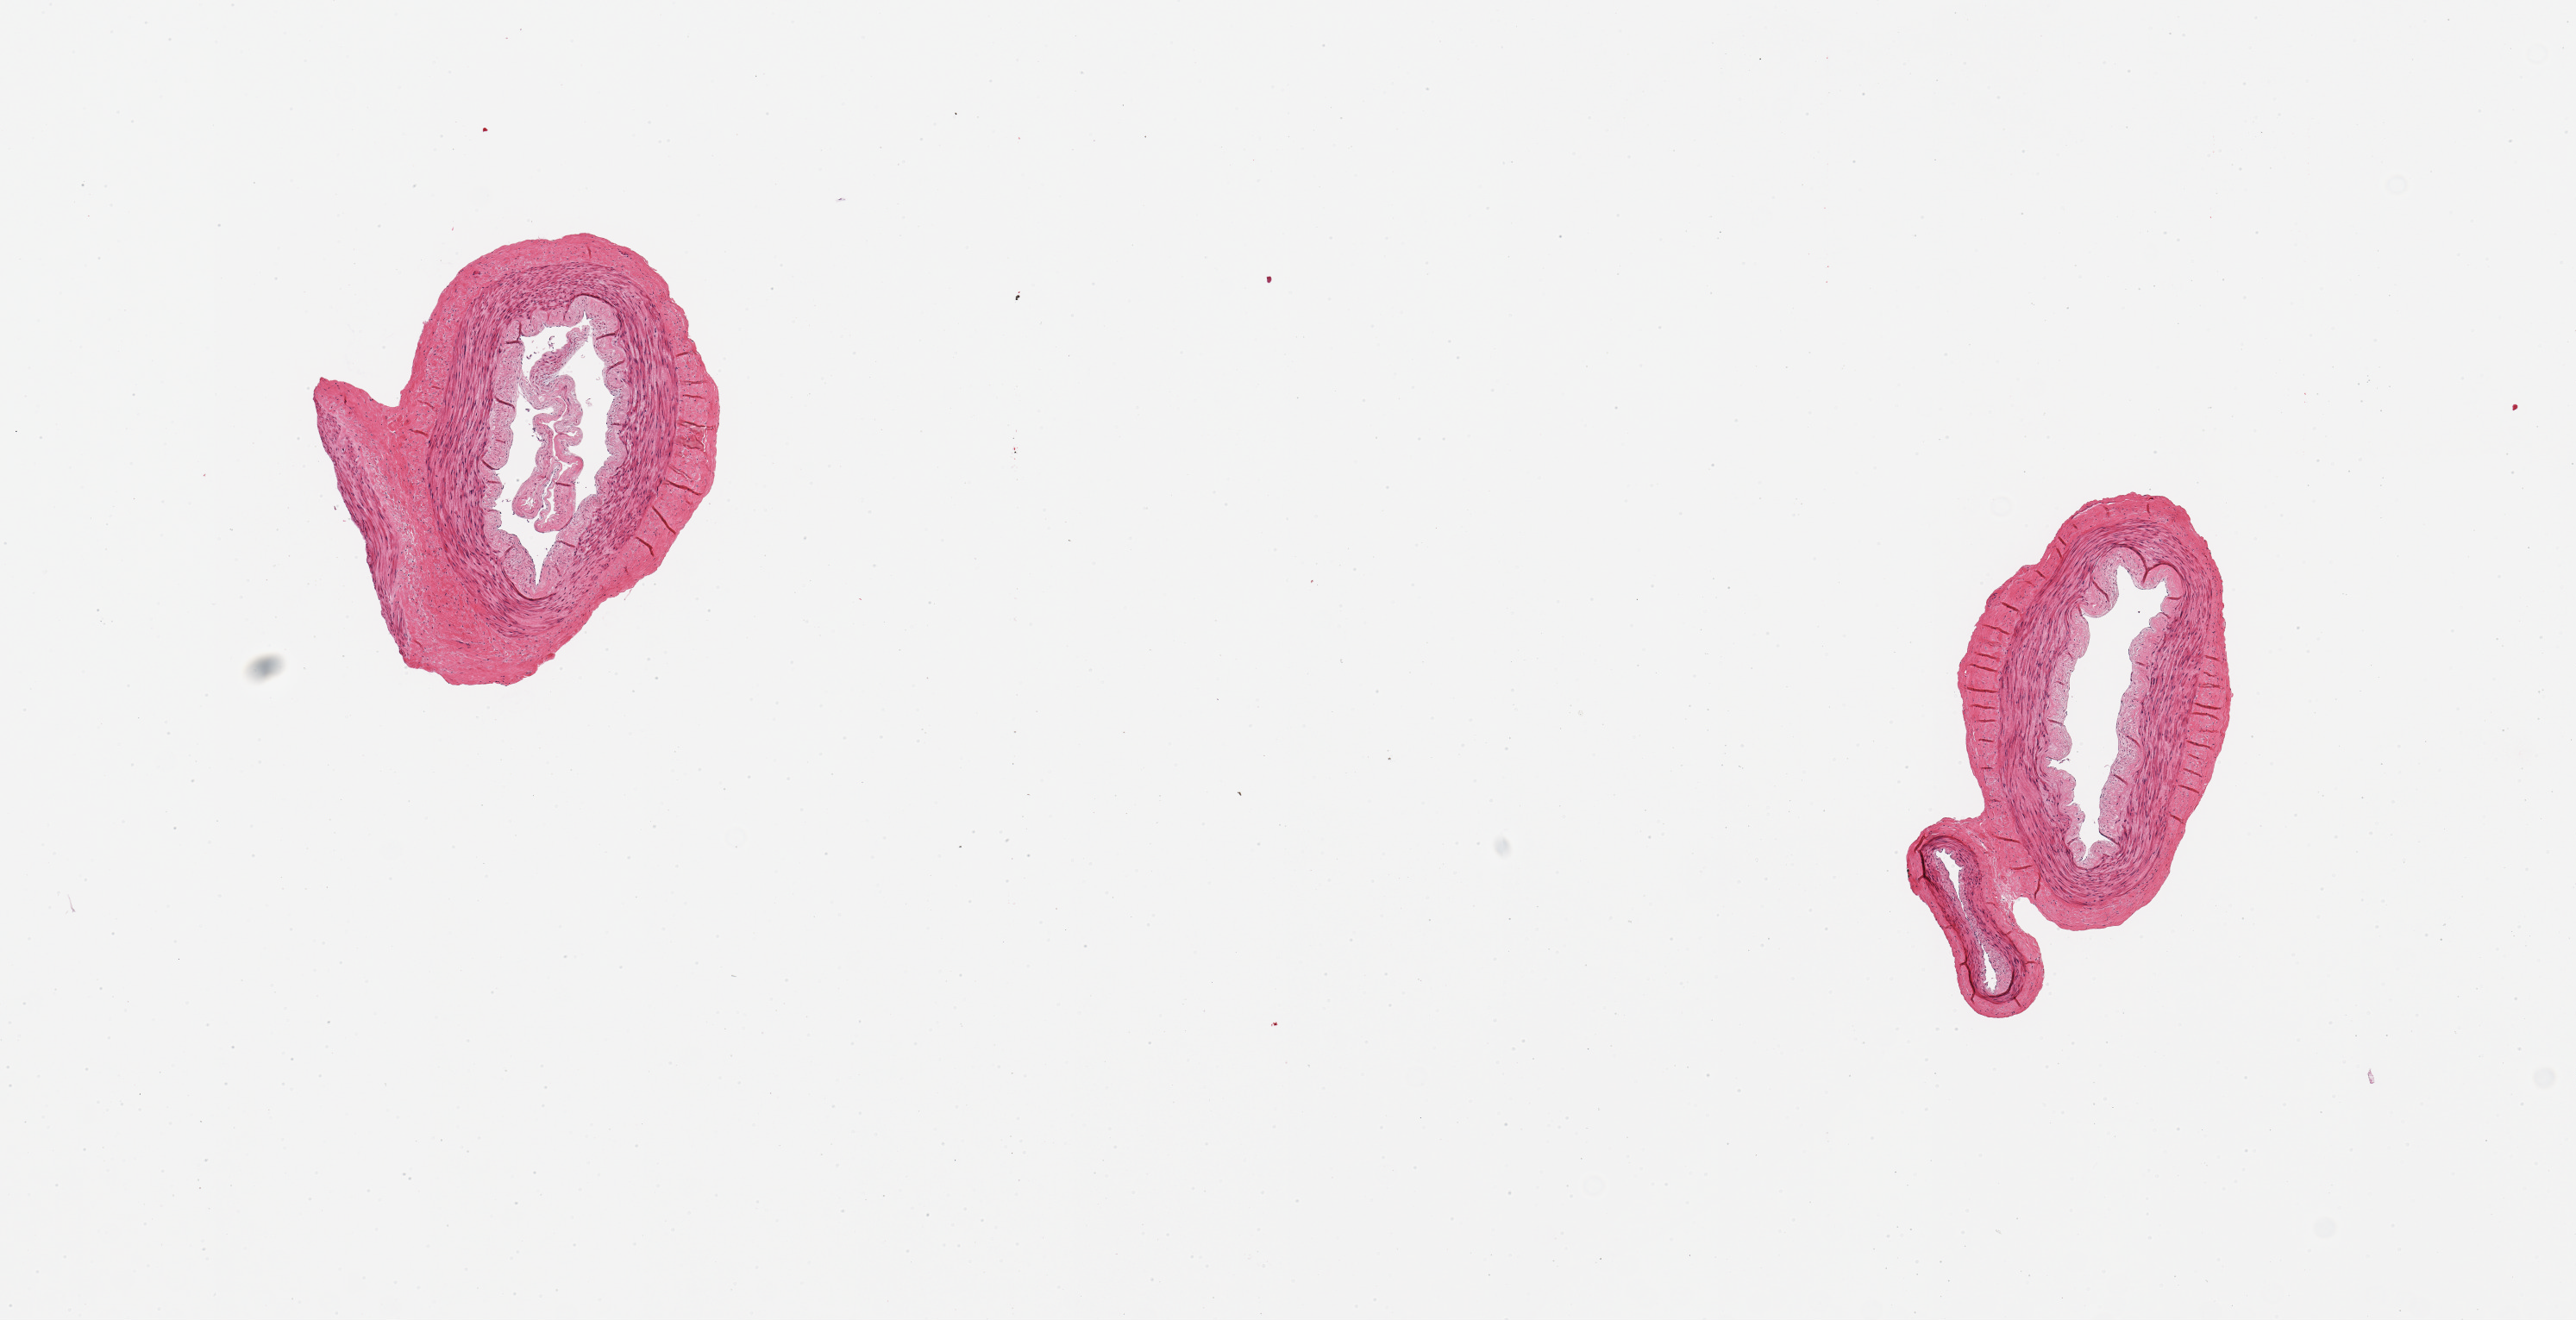
Digitized haematoxylin and eosin-stained section, a low-resolution overview of the entire scanned area, about 11.8 x 6.1 mm. PAXgene-fixed paraffin-embedded (PFPE) section. Target tissue: tibial artery. Donor tissue sample. Donor: female.
- pathologist's review note for this sample: 2 pieces; well trimmed; no lesions